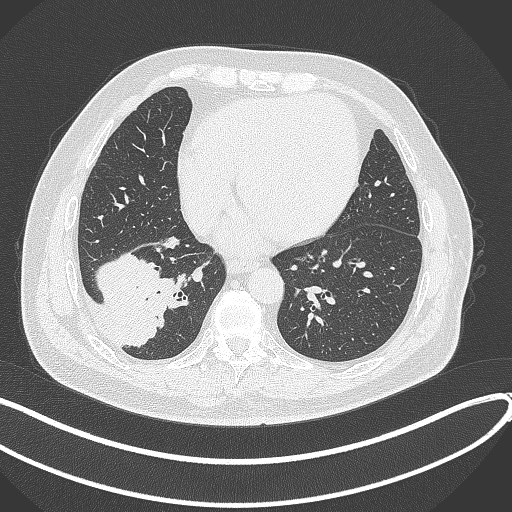
Chest CT, one axial slice. Slice 121 of 360 in the series (ordered by position). Reconstruction kernel B70f. 120 kVp. Lung window (W 1500 / L -600 HU). 512 × 512 image matrix, field of view 400 × 400 mm. Patient: male, 59 years.
Annotated regions visible in this slice (bounding box drawn by a radiologist):
- lung tumour (recorded histology: adenocarcinoma): bounding box [x1, y1, x2, y2] px = [92, 249, 177, 349]